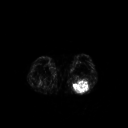
FDG PET of an extremity soft-tissue mass (from a PET/CT study), one axial slice; position 183 of 267 along the scan axis; 128 × 128 image matrix, field of view 500 × 500 mm. Male patient, age 54 years. Case-level facts recorded for this patient, not image findings: histological type: synovial sarcoma; site of the primary tumour: left poplietal fossa.
Annotated regions visible in this slice (expert contour drawn on MRI and transferred to this co-registered scan by the dataset authors):
- gross tumour volume (mass): bounding box (x1, y1, x2, y2) in pixels: (72, 80, 91, 93)